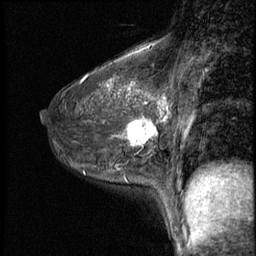
Breast MRI (dynamic contrast-enhanced), one sagittal slice; slice 34 of 50 in the series (ordered by position); 3 images stored at this slice position (order not interpretable as contrast timing); 1.5 T; TE 4.2 ms, TR 8.7 ms; 2.5 mm slice thickness; 256 × 256 image matrix, field of view 180 × 180 mm. Female patient, age 43 years. From the clinical record (not read from this slice): setting: breast cancer imaged before/during neoadjuvant chemotherapy; receptor status: HR-positive, HER2-negative.
Annotated regions visible in this slice (semi-automatically segmented with operator editing):
- analysis volume of interest (the breast-tissue region the enhancement analysis was run in; not a lesion): bounding box (x1, y1, x2, y2) in pixels: (122, 109, 159, 155)
- tumour enhancement mask (voxels above the 140 % enhancement threshold inside the analysis volume of interest): (127, 118, 157, 146)